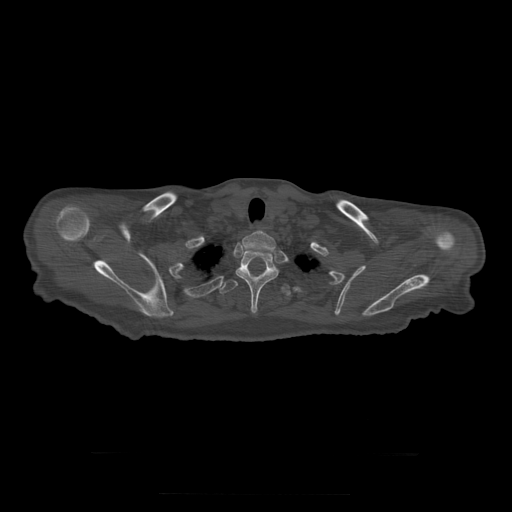
CT including the spine, one axial slice; bone window (W 1800 / L 400 HU); 1.25 mm slice thickness; 512 × 512 image matrix, field of view 510 × 510 mm. Patient age 73 years. Case-level facts recorded for this patient, not image findings: primary cancer: prostate.
Annotated regions visible in this slice (semi-automatically segmented with operator editing):
- T1 vertebra: bounding box [x1, y1, x2, y2] px = [242, 231, 276, 252]
- T2 vertebra: [236, 251, 279, 314]
- T3 vertebra: [220, 280, 291, 296]